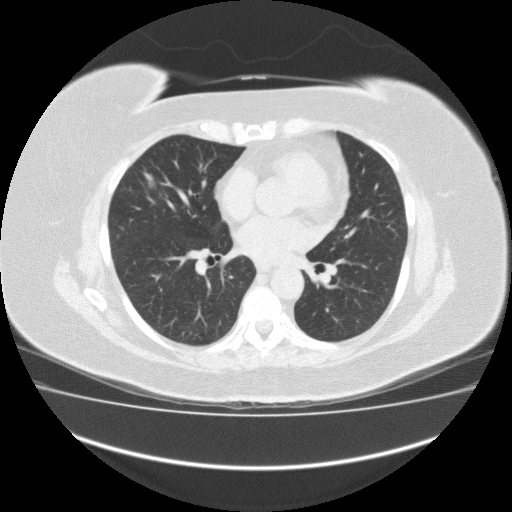
Low-dose screening chest CT, one axial slice; slice 83 of 162 in the series (ordered by position); lung window (W 1500 / L -600 HU); 2 mm slice thickness; 512 × 512 image matrix.
Structures marked on this image (outlined manually by an expert reader):
- lesion 1 (tumor, middle lobe of right lung): bounding box [x1, y1, x2, y2] px = [144, 173, 154, 186]